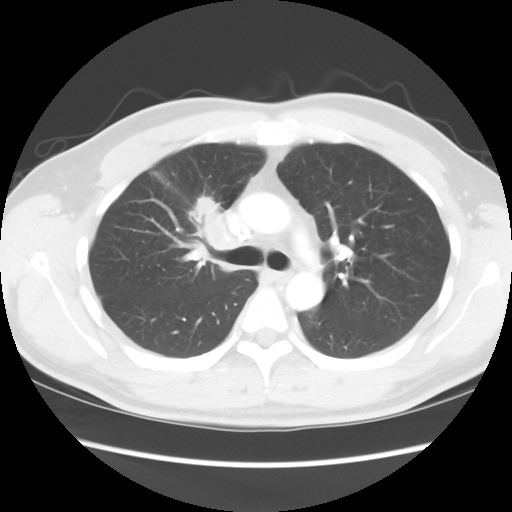
Chest CT, one axial slice; slice 61 of 80 in the series (ordered by position); reconstruction kernel STANDARD; lung window (W 1500 / L -600 HU); 5 mm slice thickness; 512 × 512 image matrix, field of view 360 × 360 mm. Patient: male, 35 years. Case-level facts recorded for this patient, not image findings: clinical TNM (as recorded): T1c N1 M1b.
Annotated regions visible in this slice (rectangle marked by the reading radiologist):
- lung tumour (recorded histology: adenocarcinoma): bounding box (x1, y1, x2, y2) in pixels: (191, 196, 236, 254)